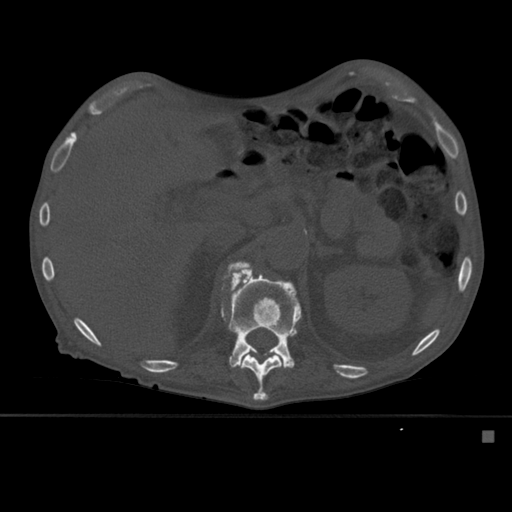
CT including the spine, one axial slice. Slice 266 of 527 in the series (ordered by position). Bone window (W 1800 / L 400 HU). 1.5 mm slice thickness. 512 × 512 image matrix. Male patient, age 78 years. Case-level facts recorded for this patient, not image findings: primary cancer: prostate.
Annotated regions visible in this slice (semi-automatic segmentation, software-assisted and operator-edited):
- L1 vertebra: box from (x=221, y=273) to (x=301, y=401) px
- T12 vertebra: (x=222, y=260)–(x=282, y=401)